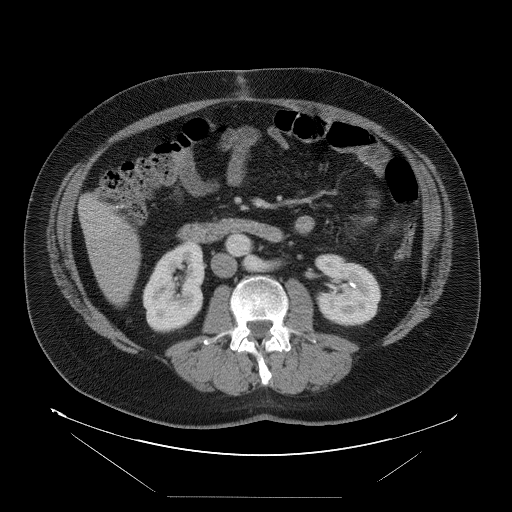
Contrast-enhanced abdominal CT, one axial slice. Position 25 of 114 along the scan axis. Soft-tissue window (W 400 / L 40 HU). 512 × 512 image matrix. Male patient, age 61 years. From the clinical record (not read from this slice): diagnosis: colorectal cancer liver metastases, imaged before liver resection; multiple liver metastases: no; largest metastasis: 6.5 cm; chemotherapy before resection: no.
Outlined on this slice (manually delineated by an expert):
- liver: bounding box [x1, y1, x2, y2] px = [81, 195, 141, 306]